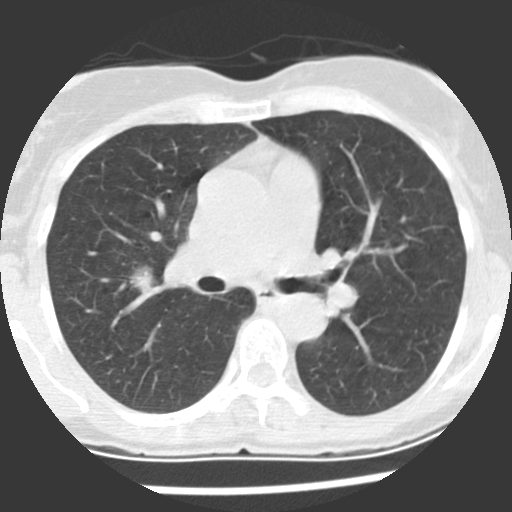
Chest CT (low-dose screening protocol), one axial image, baseline screening round, lung window (W 1500 / L -600 HU), standard (soft-tissue) reconstruction kernel (STANDARD), 120 kVp, slice 97 of 225 in the series, 512 × 512 image matrix. Female participant, aged 60 years at enrolment. Current smoker at enrolment.
• Expert reader's lesion annotation, bounding box [x1, y1, x2, y2] px = [115, 257, 171, 304].
• The screening reader recorded 2 non-calcified nodules or masses ≥4 mm on this exam (right upper lobe, right middle lobe); which of them this box marks is not recorded.
• Official screen result: positive, change unspecified: nodule(s) >= 4 mm or enlarging nodule(s), mass(es), or other non-specific abnormalities suspicious for lung cancer.
• Lung cancer was diagnosed 10 days after this screen: adenocarcinoma, NOS, right upper lobe, stage IIIA (AJCC 6th edition), 20 mm at pathology.